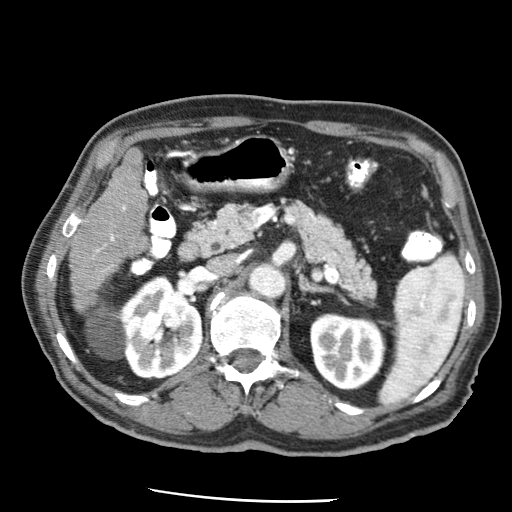
Contrast-enhanced abdominal CT (liver protocol), one axial slice. Slice 18 of 79 in the series (ordered by position). Reconstruction kernel STANDARD. 120 kVp. Soft-tissue window (W 400 / L 40 HU). 2.5 mm slice thickness. 512 × 512 image matrix, field of view 320 × 320 mm. From the clinical record (not read from this slice): diagnosis: hepatocellular carcinoma (patient treated with transarterial chemoembolisation; whether this scan precedes or follows treatment is not stated here); TNM stage (as recorded): Stage-IIIA; Child-Pugh class: A; tumour differentiation: moderately differentiated; tumour nodularity: multinodular.
Outlined on this slice (semi-automatic segmentation, software-assisted and operator-edited):
- liver parenchyma outside the tumour (the mass and vessels are separate outlines, so this box may not span the whole liver): bounding box (x1, y1, x2, y2) in pixels: (70, 148, 146, 310)
- liver vessels: (96, 206, 126, 269)